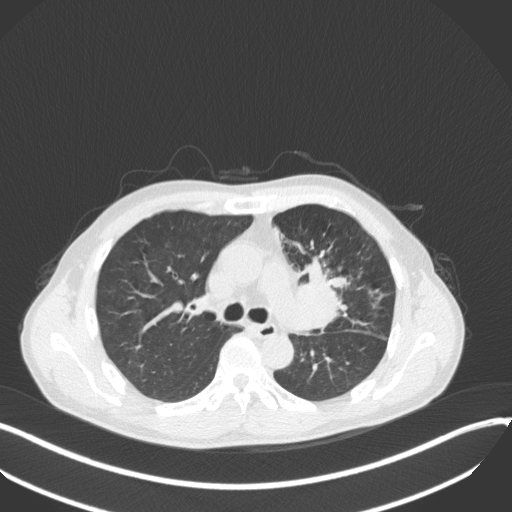
Chest CT, one axial slice; position 216 of 411 along the scan axis; reconstruction kernel B31f; 120 kVp; lung window (W 1500 / L -600 HU); 1 mm slice thickness; 512 × 512 image matrix, field of view 400 × 400 mm. Patient: male, 56 years. From the clinical record (not read from this slice): clinical TNM (as recorded): T2a N0 M0.
Outlined on this slice (rectangle marked by the reading radiologist):
- lung tumour (recorded histology: squamous cell carcinoma): bounding box (x1, y1, x2, y2) in pixels: (291, 252, 349, 339)